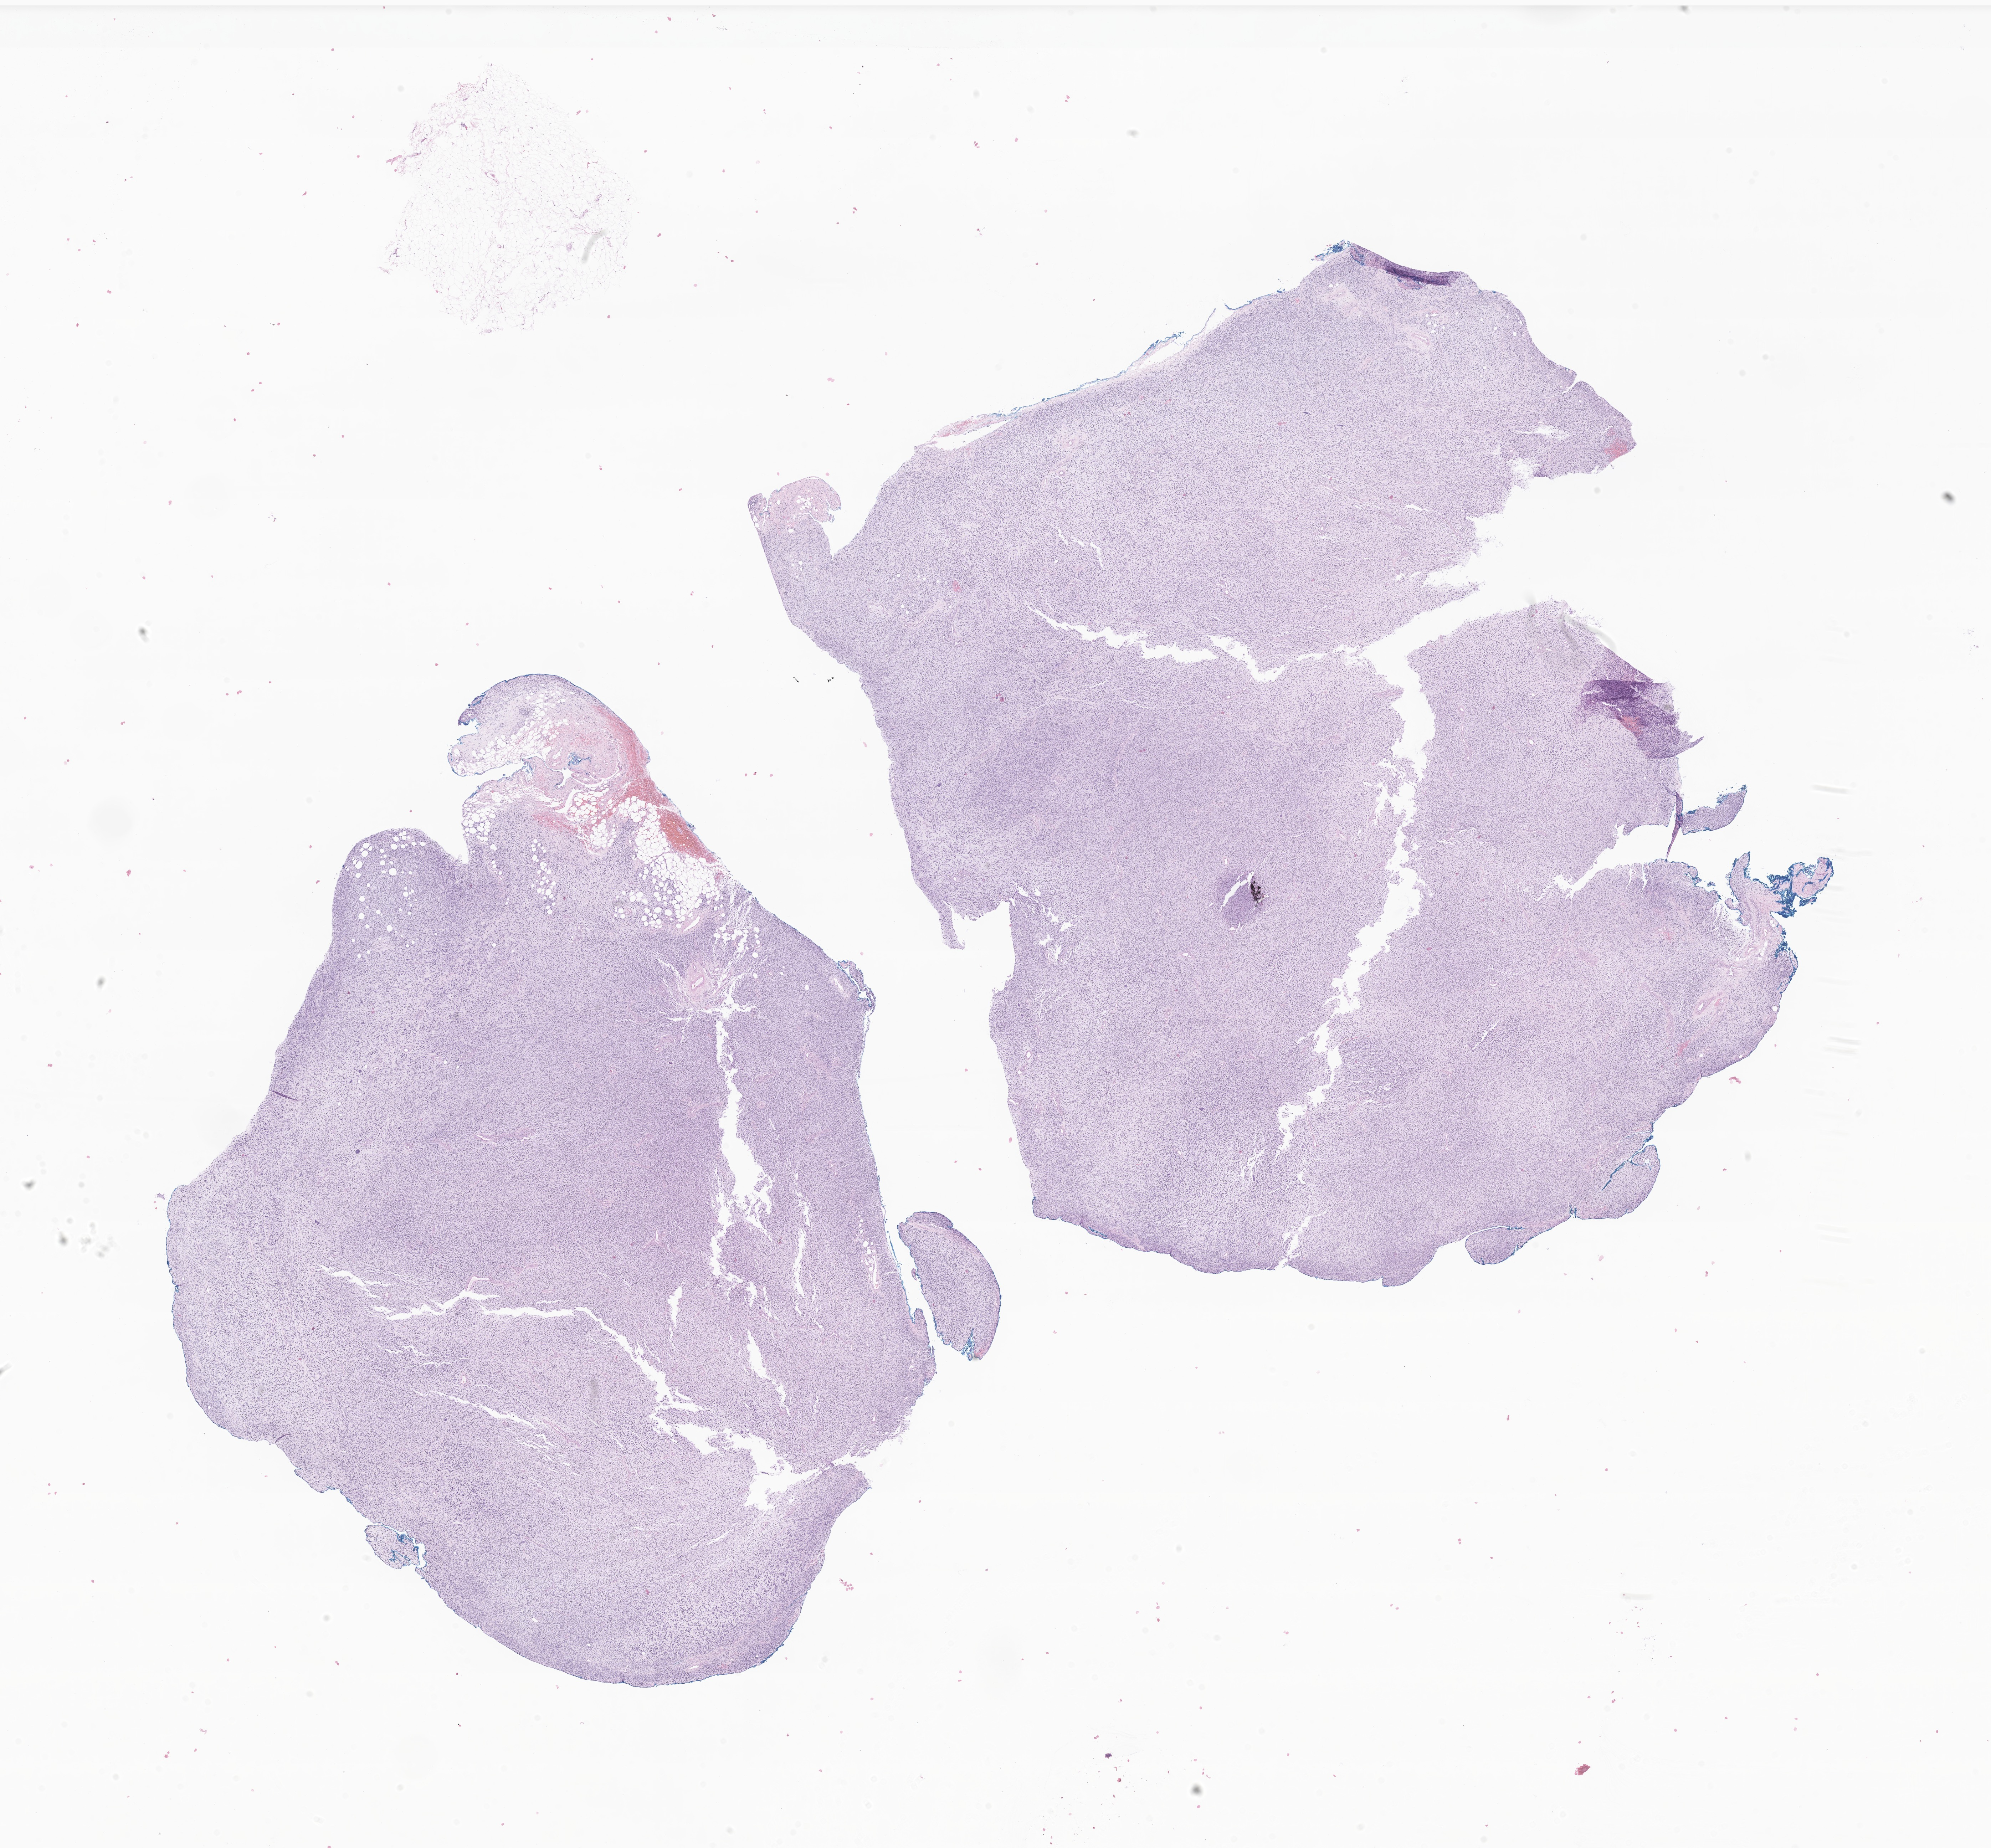
H&E whole-slide image of tumor tissue from the orbit, a low-resolution overview of the entire scanned area, about 23.5 x 21.9 mm, FFPE section. Patient: male, age 109 months.
Recorded diagnosis: Rhabdomyosarcoma, NOS.